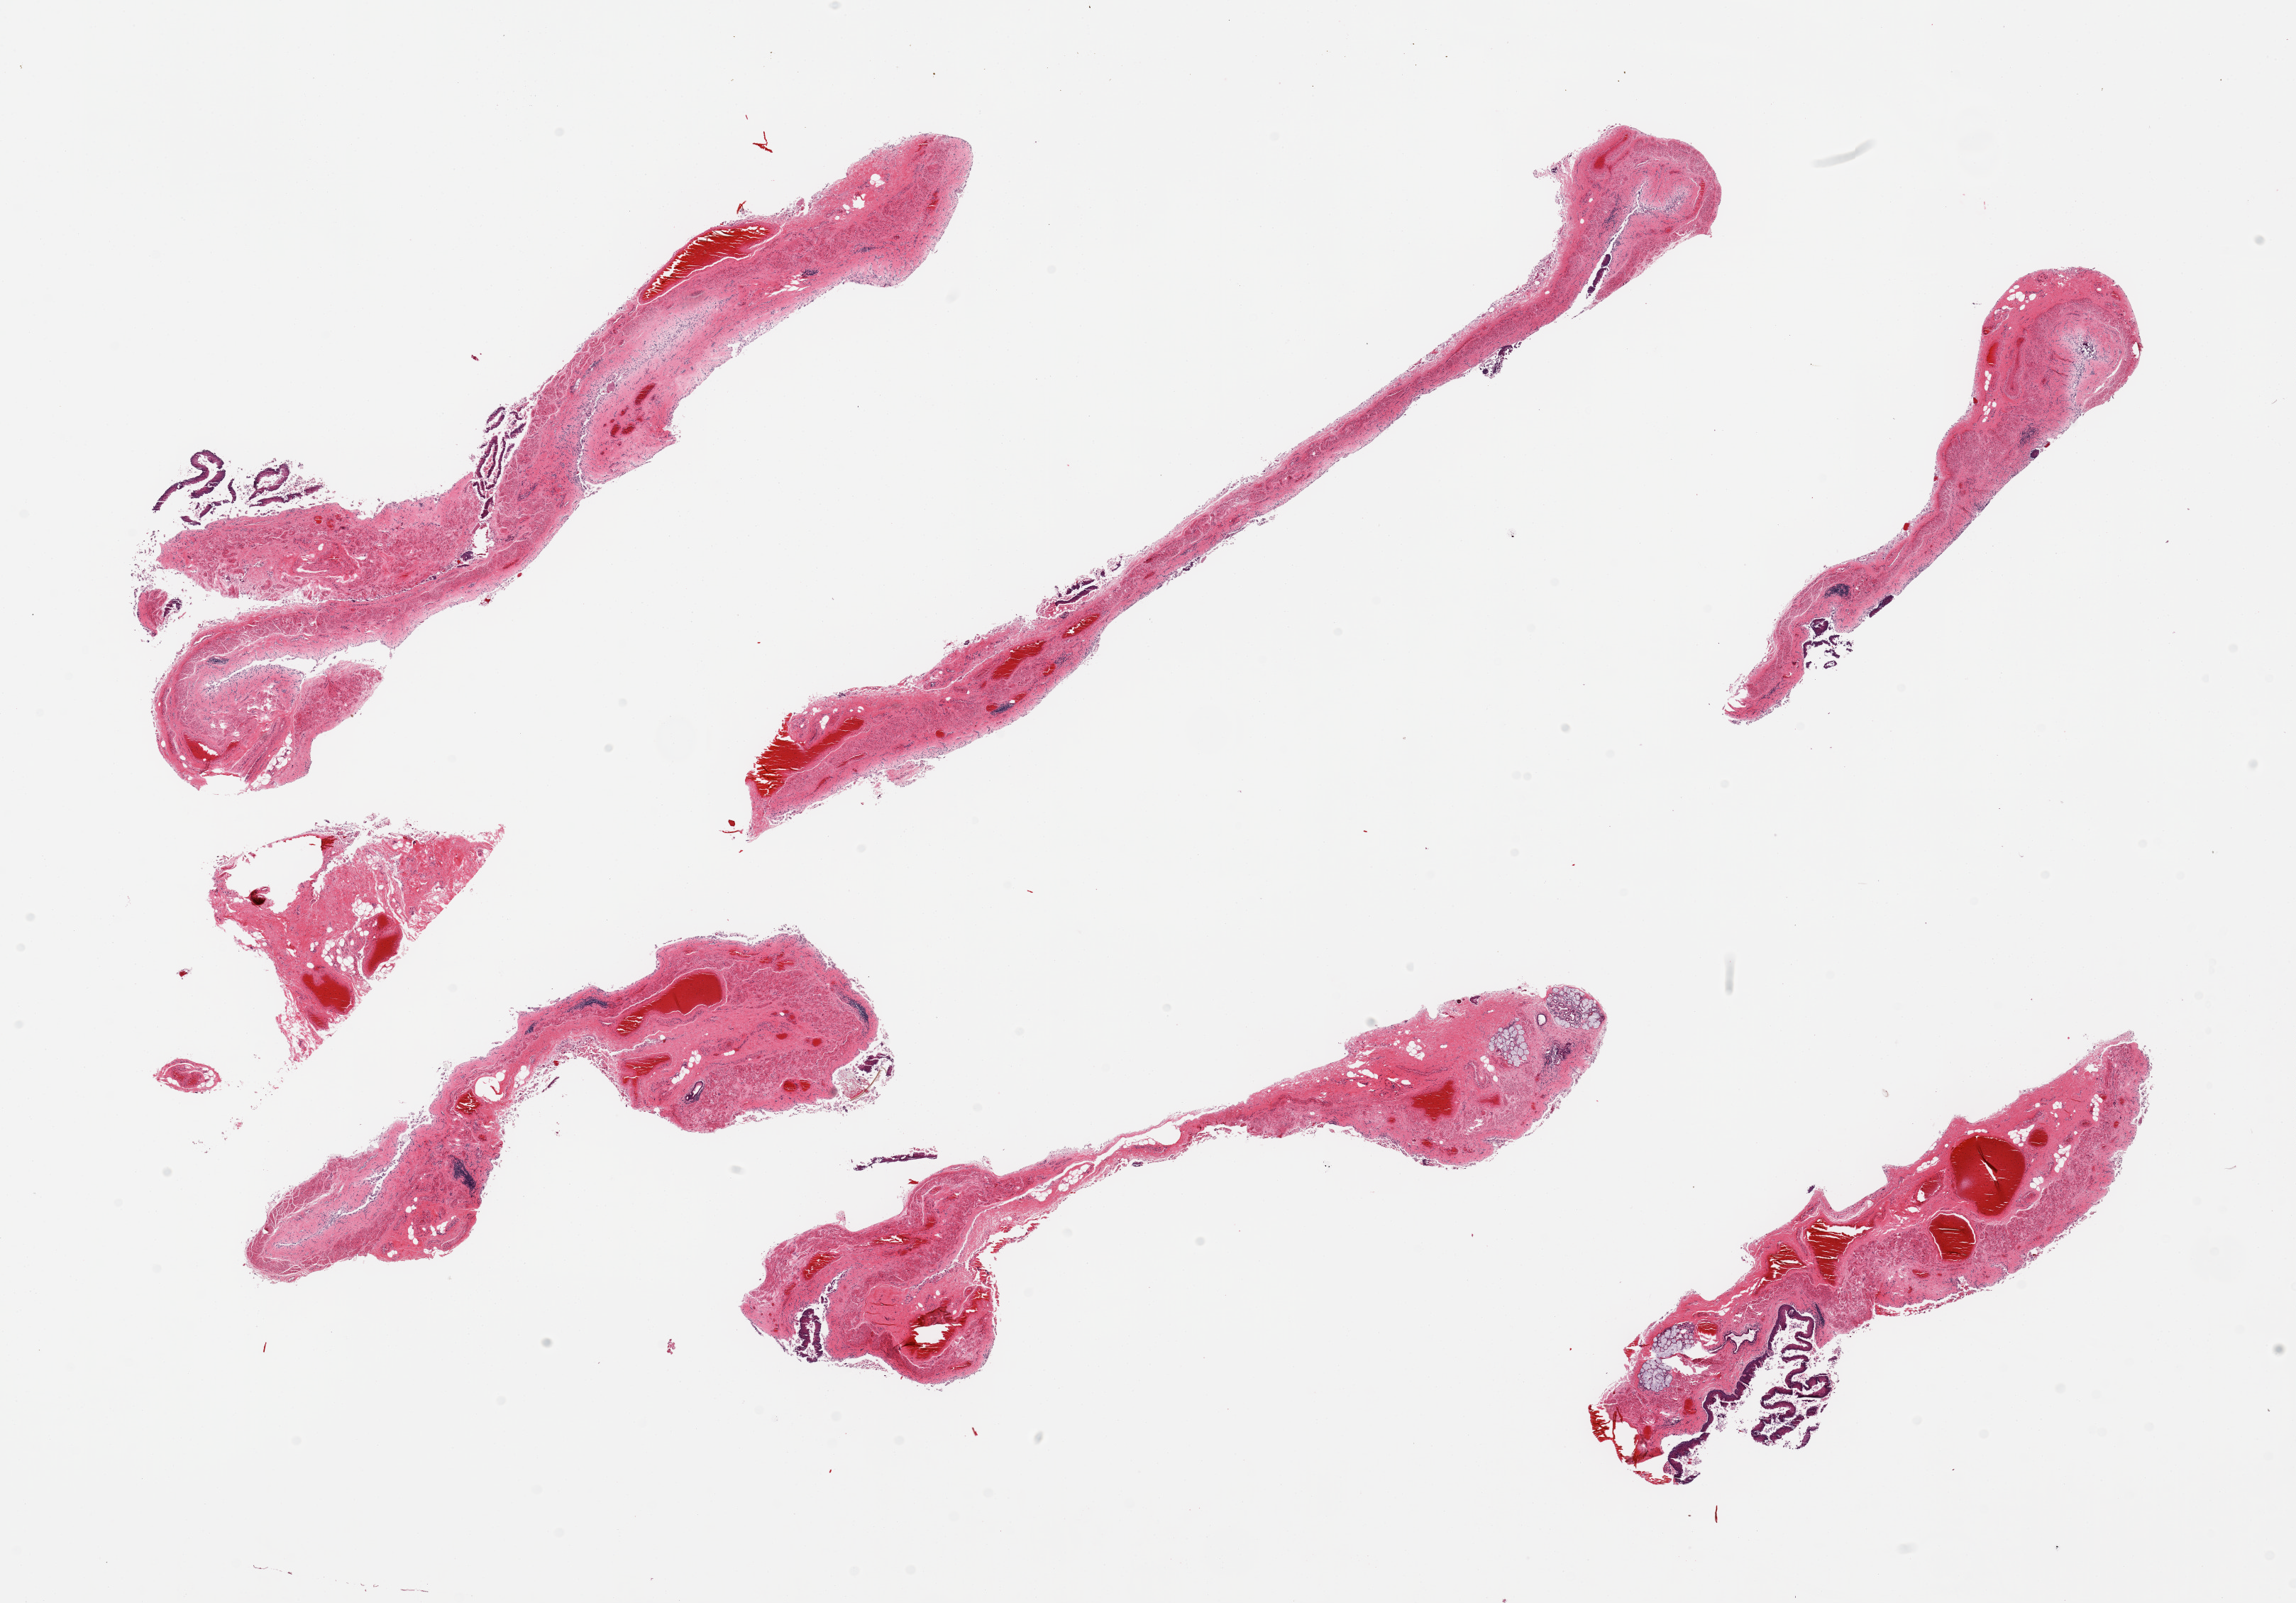
H&E whole-slide image — whole scanned area (about 25.6 x 17.9 mm) shown as a low-resolution overview, PAXgene-fixed paraffin-embedded (PFPE) section, sampled site (target tissue): esophageal mucous membrane, tissue donor sample. Donor: male.
• pathologist's review note for this sample: 6 pieces; too autolyzed, surface sloughed